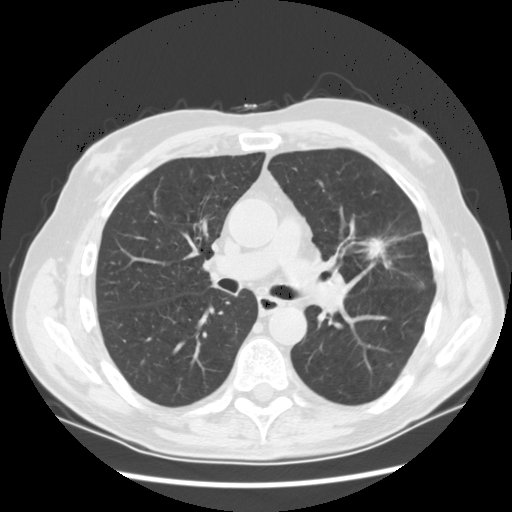
Axial slice from a low-dose chest CT screening exam; first (baseline) screen; lung window (W 1500 / L -600 HU); standard (soft-tissue) reconstruction kernel (STANDARD); 120 kVp; slice 55 of 132 in the series; 512 × 512 image matrix, field of view 380 × 380 mm. Male participant, aged 65 years at enrolment. Current smoker at enrolment.
Lesion marked by an expert reader, bounding box [x1, y1, x2, y2] px = [350, 222, 415, 289]. Screening reader's record for this exam (one nodule recorded; not confirmed to be the boxed lesion): non-calcified nodule or mass ≥4 mm, left upper lobe, 37 × 27 mm, spiculated (stellate) margins, soft tissue attenuation. Later outcome: lung cancer diagnosed 56 days after this screen — non-small cell carcinoma, poorly differentiated (G3), stage IA (AJCC 6th edition).